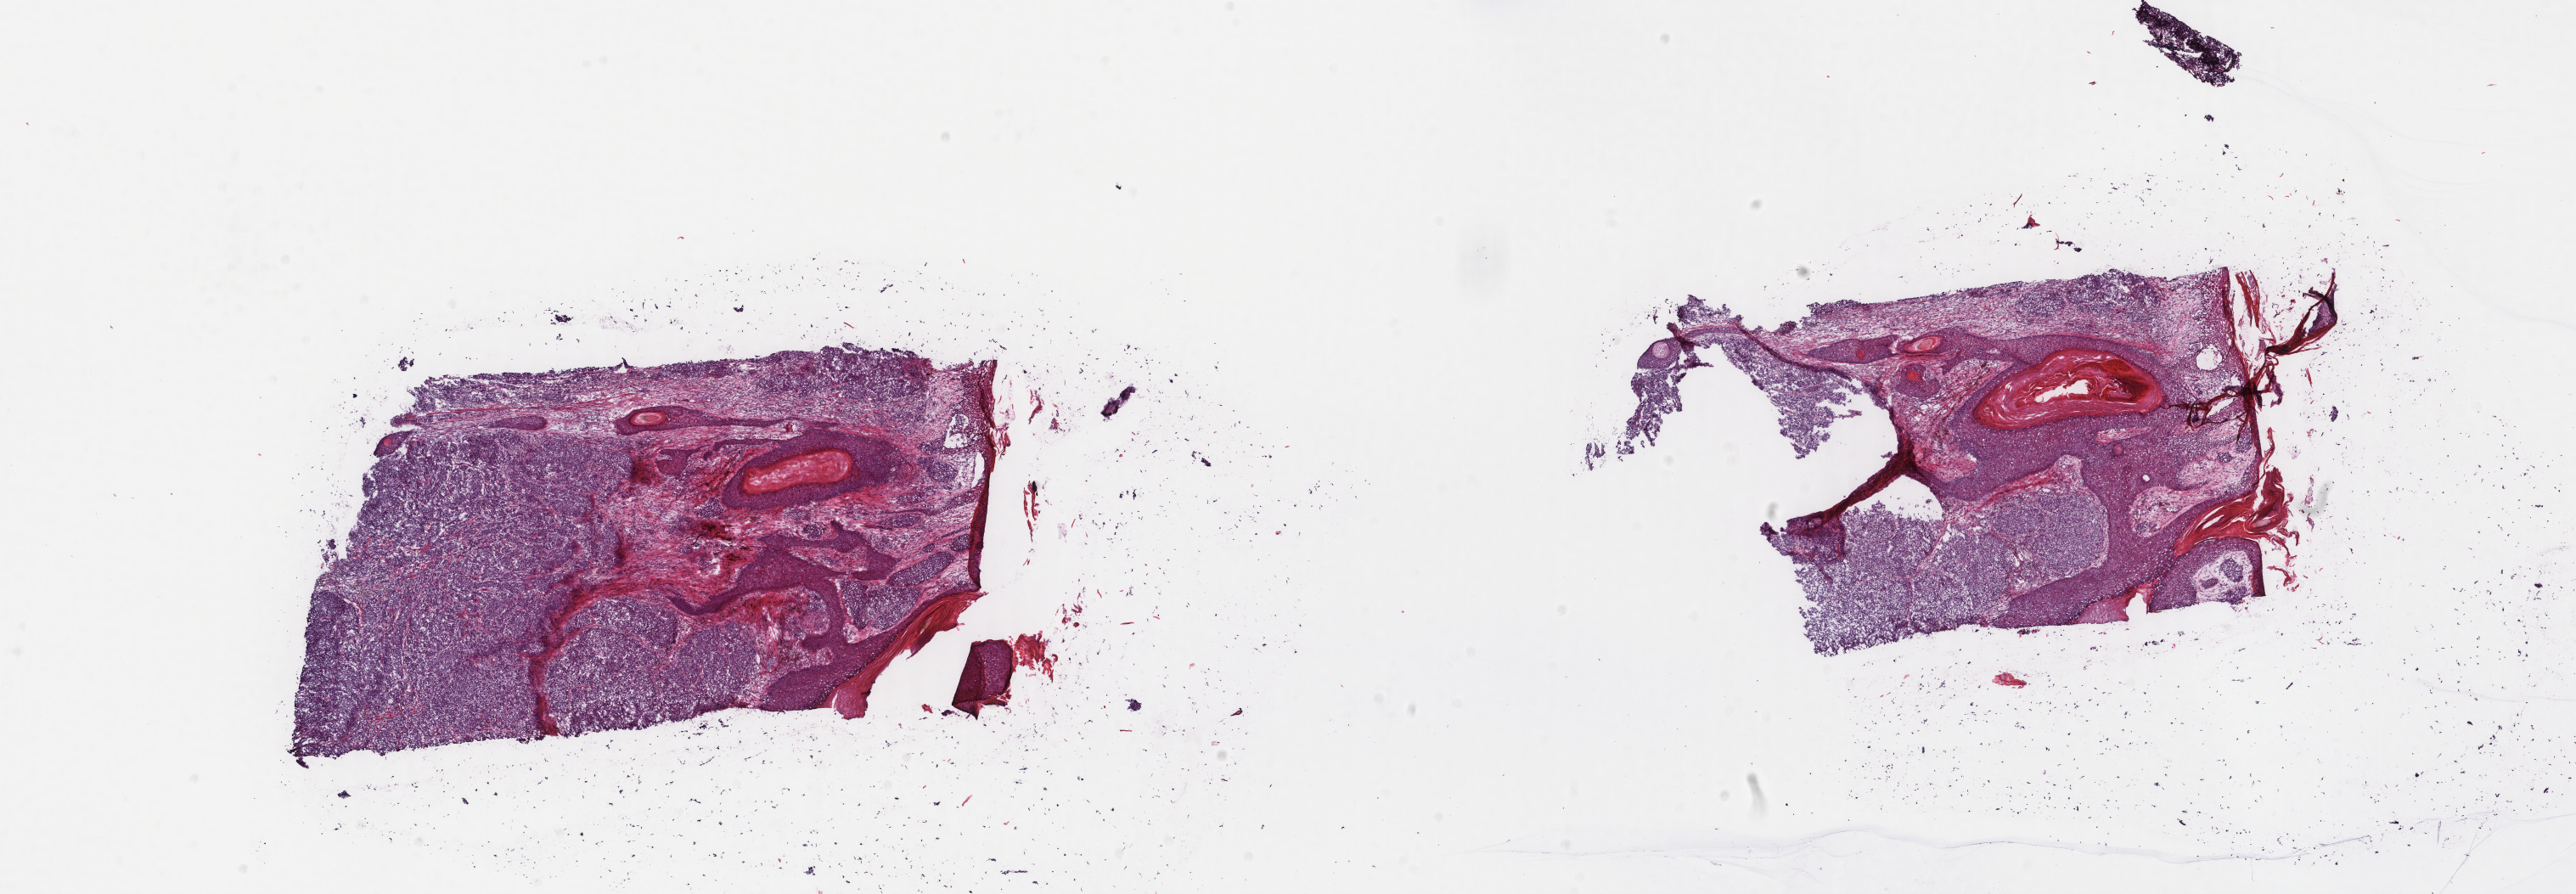
H&E-stained whole-slide image, shown as a low-resolution overview of the whole scanned area (about 24.1 x 8.4 mm, from a 40x scan); frozen section from the top of the tissue portion; skin, primary tumour sample. Female patient; age at initial diagnosis 79 years. Pathologist review of this section (percent, as recorded): tumour cells 75%, tumour nuclei 88%, normal cells 20%, stromal cells 5%, necrosis 0%. Infiltration values recorded for this section: lymphocyte infiltration 0%, monocyte infiltration 0%, neutrophil infiltration 0%.
Pathologic diagnosis: Malignant melanoma, NOS.